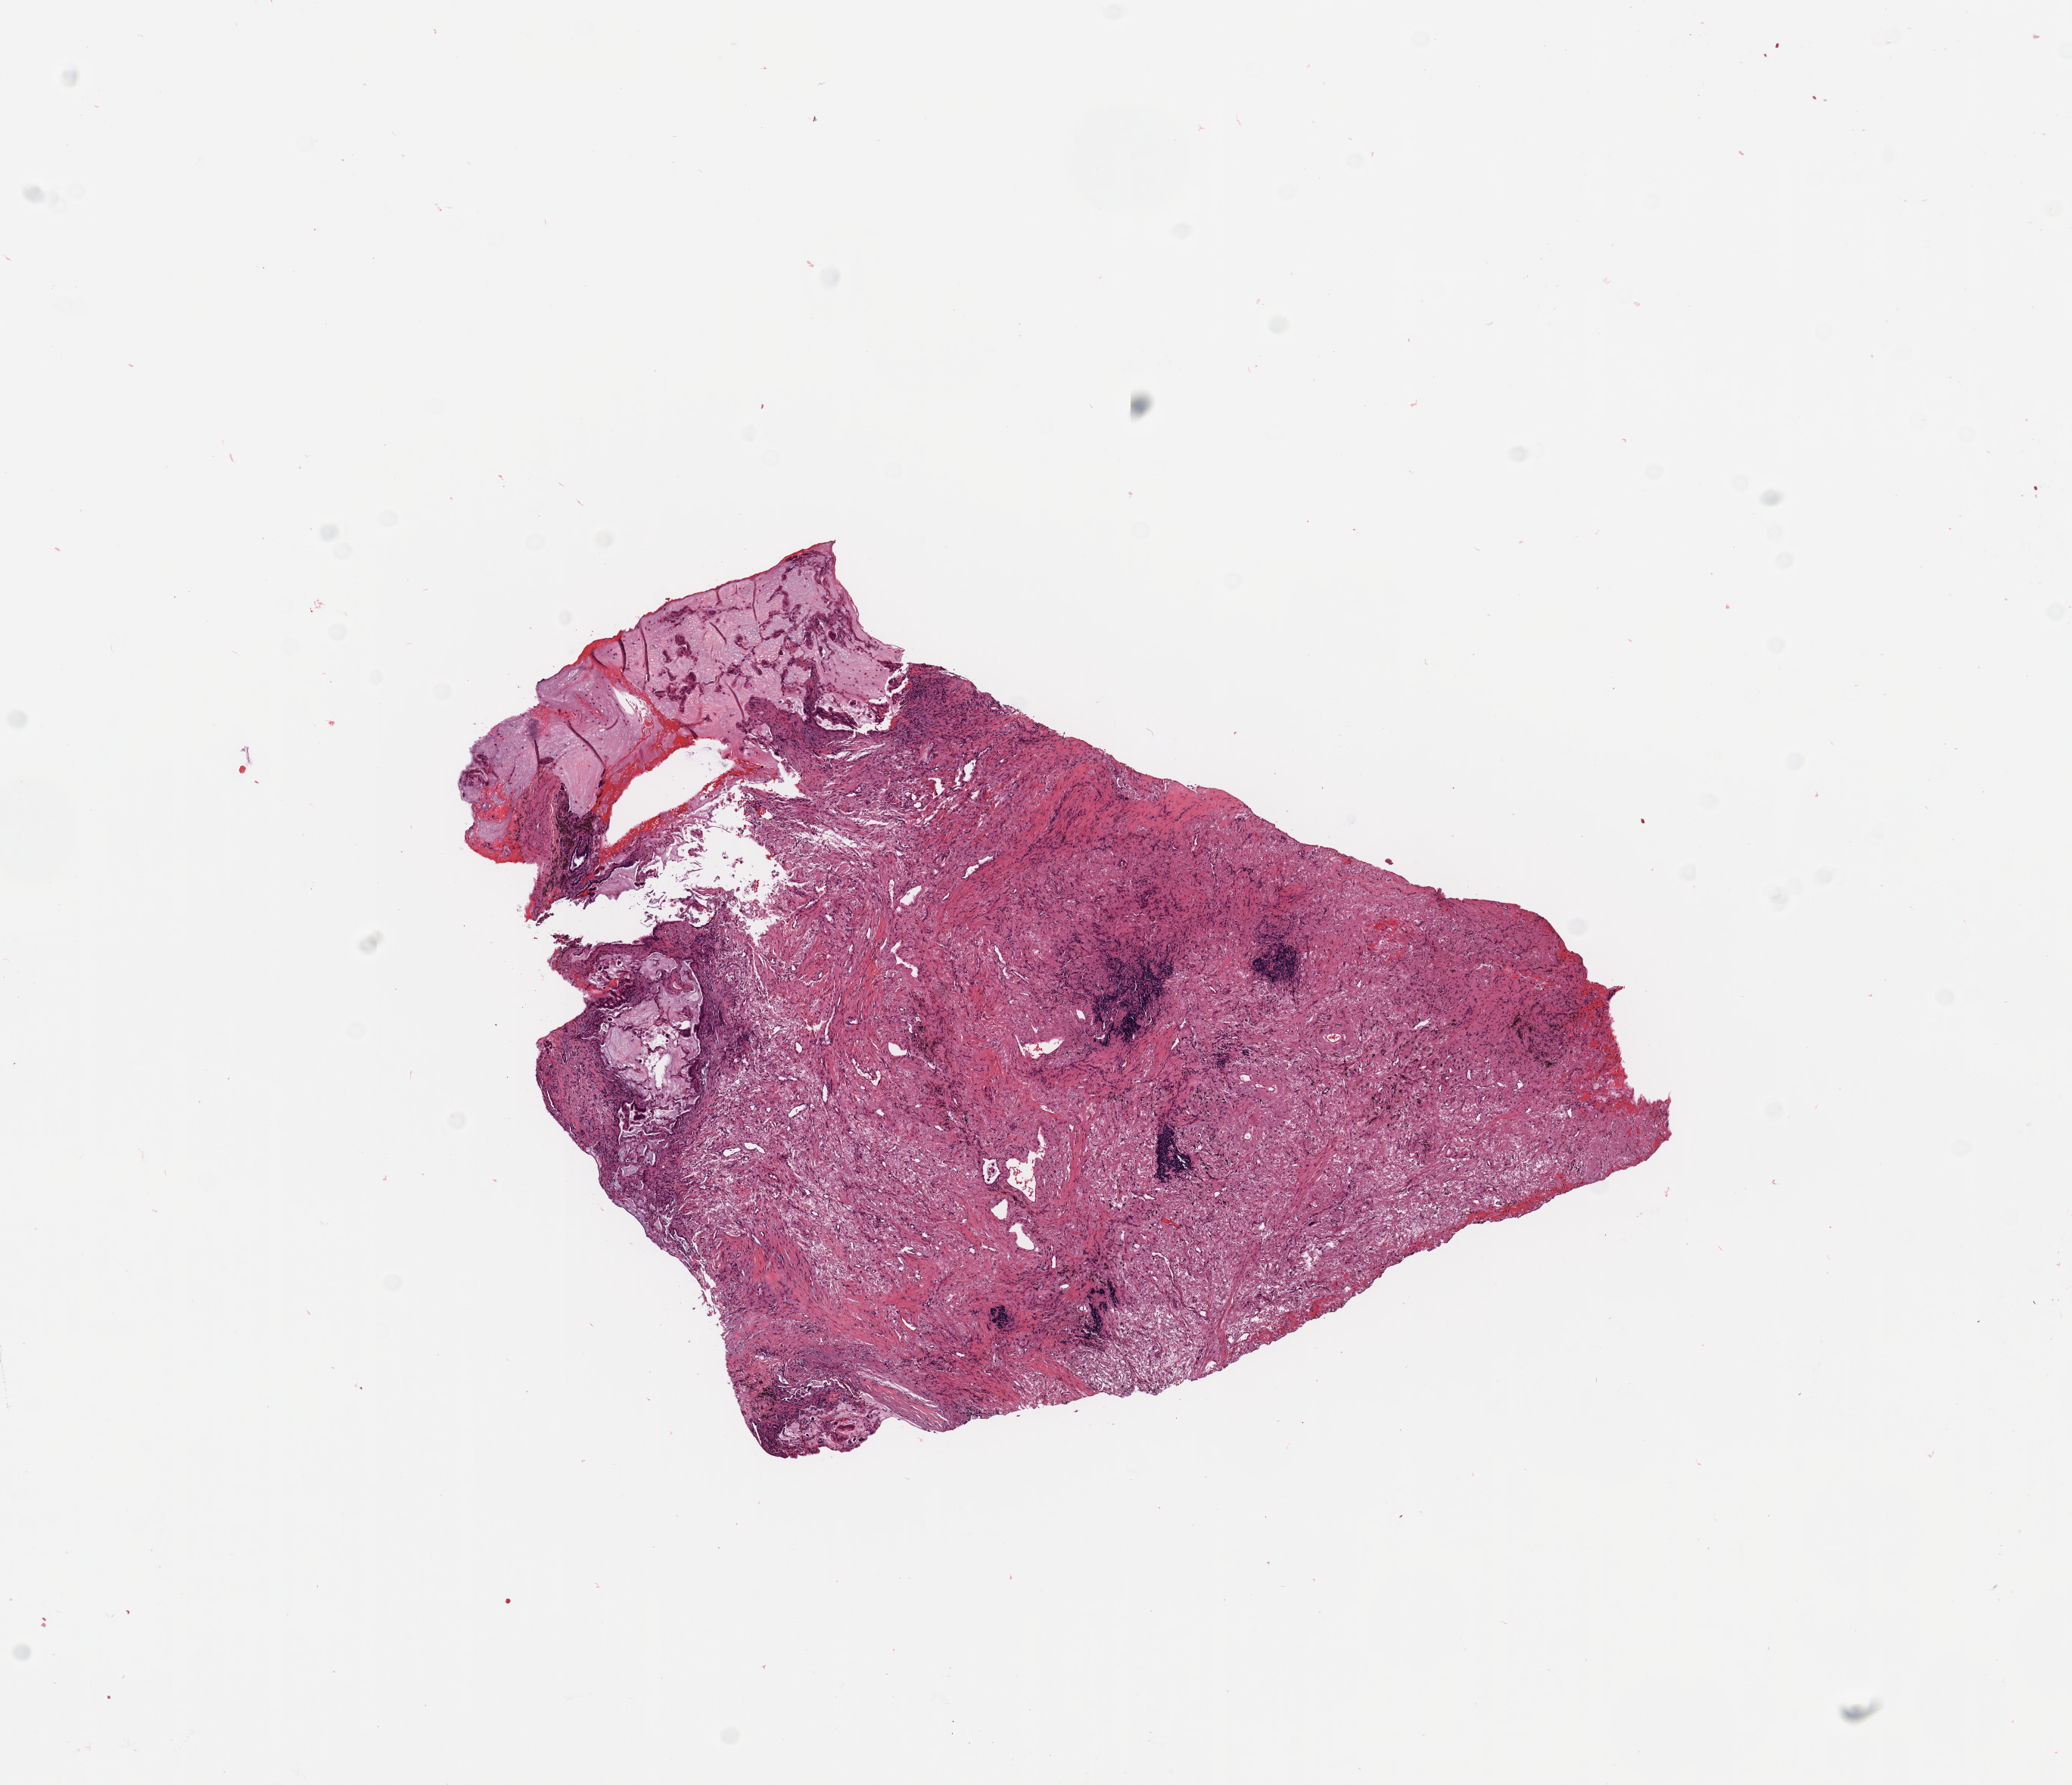
Digitized H&E tissue section (whole slide), low-resolution overview of the scanned area, about 10.8 x 9.3 mm, tumour tissue sample, lung. 65-year-old male patient. Histologic grade: G2 (moderately differentiated).
Histologic diagnosis: Adenocarcinoma, NOS. AJCC pathologic stage: IB. Primary tumour site (as recorded): left upper lobe.